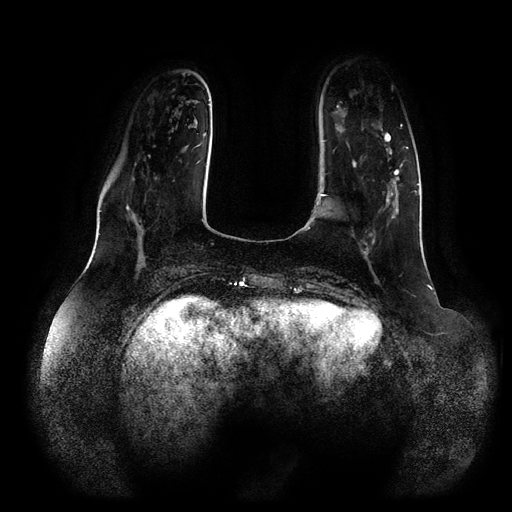
Breast MRI (dynamic contrast-enhanced, multi-phase), one axial slice. Slice 26 of 116 in the series (ordered by position). Dynamic contrast-enhanced series, time point 2 of 5 at this slice position (early post-contrast). 1.5 T. TE 2.5 ms, TR 5.2 ms. 512 × 512 image matrix. Patient: female, 66 years.
Outlined on this slice (semi-automatic segmentation, software-assisted and operator-edited):
- breast lesion (labelled 'tumour' in the annotation; benign lesions carry a separate 'benign' label): bounding box (x1, y1, x2, y2) in pixels: (381, 129, 403, 227)